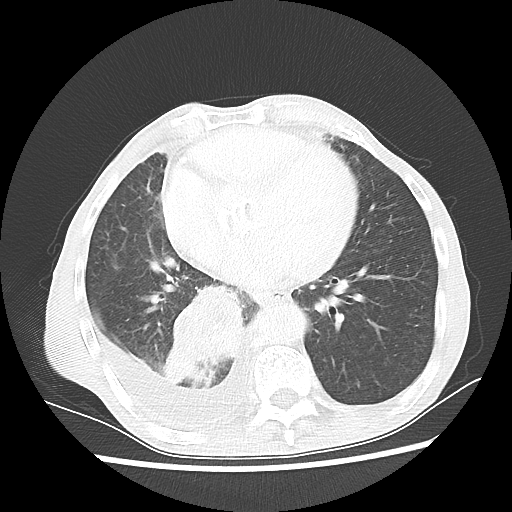
Chest CT, one axial slice; slice 24 of 60 in the series (ordered by position); reconstruction kernel LUNG; lung window (W 1500 / L -600 HU); 512 × 512 image matrix, field of view 335 × 335 mm. Patient: male, 76 years. Case-level facts recorded for this patient, not image findings: clinical TNM (as recorded): T3 N3 M1a; histopathological grade: G3.
Annotated regions visible in this slice (bounding box drawn by a radiologist):
- lung tumour (recorded histology: squamous cell carcinoma): bounding box <161,277,248,390> (left, top, right, bottom; pixels)